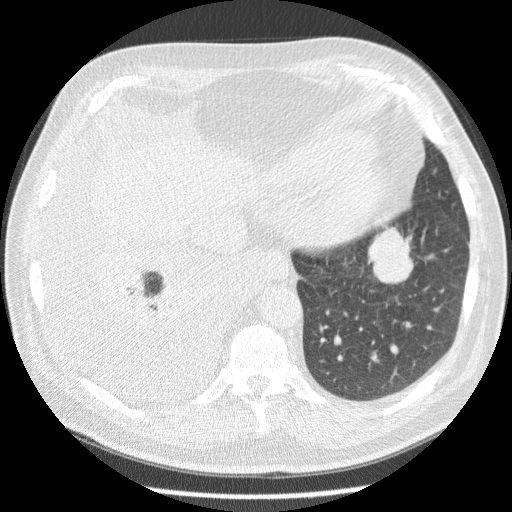
Low-dose screening chest CT, one axial slice; slice 54 of 180 in the series (ordered by position); 120 kVp; lung window (W 1500 / L -600 HU); 2.5 mm slice thickness; 512 × 512 image matrix, field of view 355 × 355 mm.
Structures marked on this image (expert manual segmentation):
- lesion 1 (tumor, lower lobe of left lung): bounding box (x1, y1, x2, y2) in pixels: (368, 227, 414, 283)